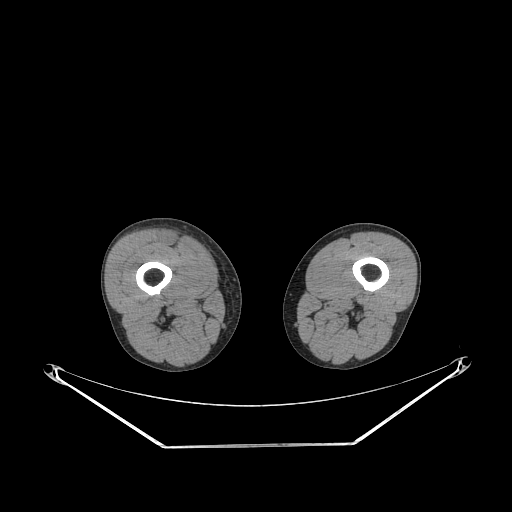
CT of an extremity soft-tissue mass (from a PET/CT study), one axial slice. Position 226 of 311 along the scan axis. 140 kVp. Soft-tissue window (W 400 / L 40 HU). 3.75 mm slice thickness. 512 × 512 image matrix, field of view 500 × 500 mm. Male patient. From the clinical record (not read from this slice): histological type: pleiomorphic leiomyosarcoma; grade: intermediate; site of the primary tumour: right thigh.
Outlined on this slice (expert contour drawn on MRI and transferred to this co-registered scan by the dataset authors):
- gross tumour volume including surrounding oedema: box from (x=162, y=233) to (x=181, y=247) px